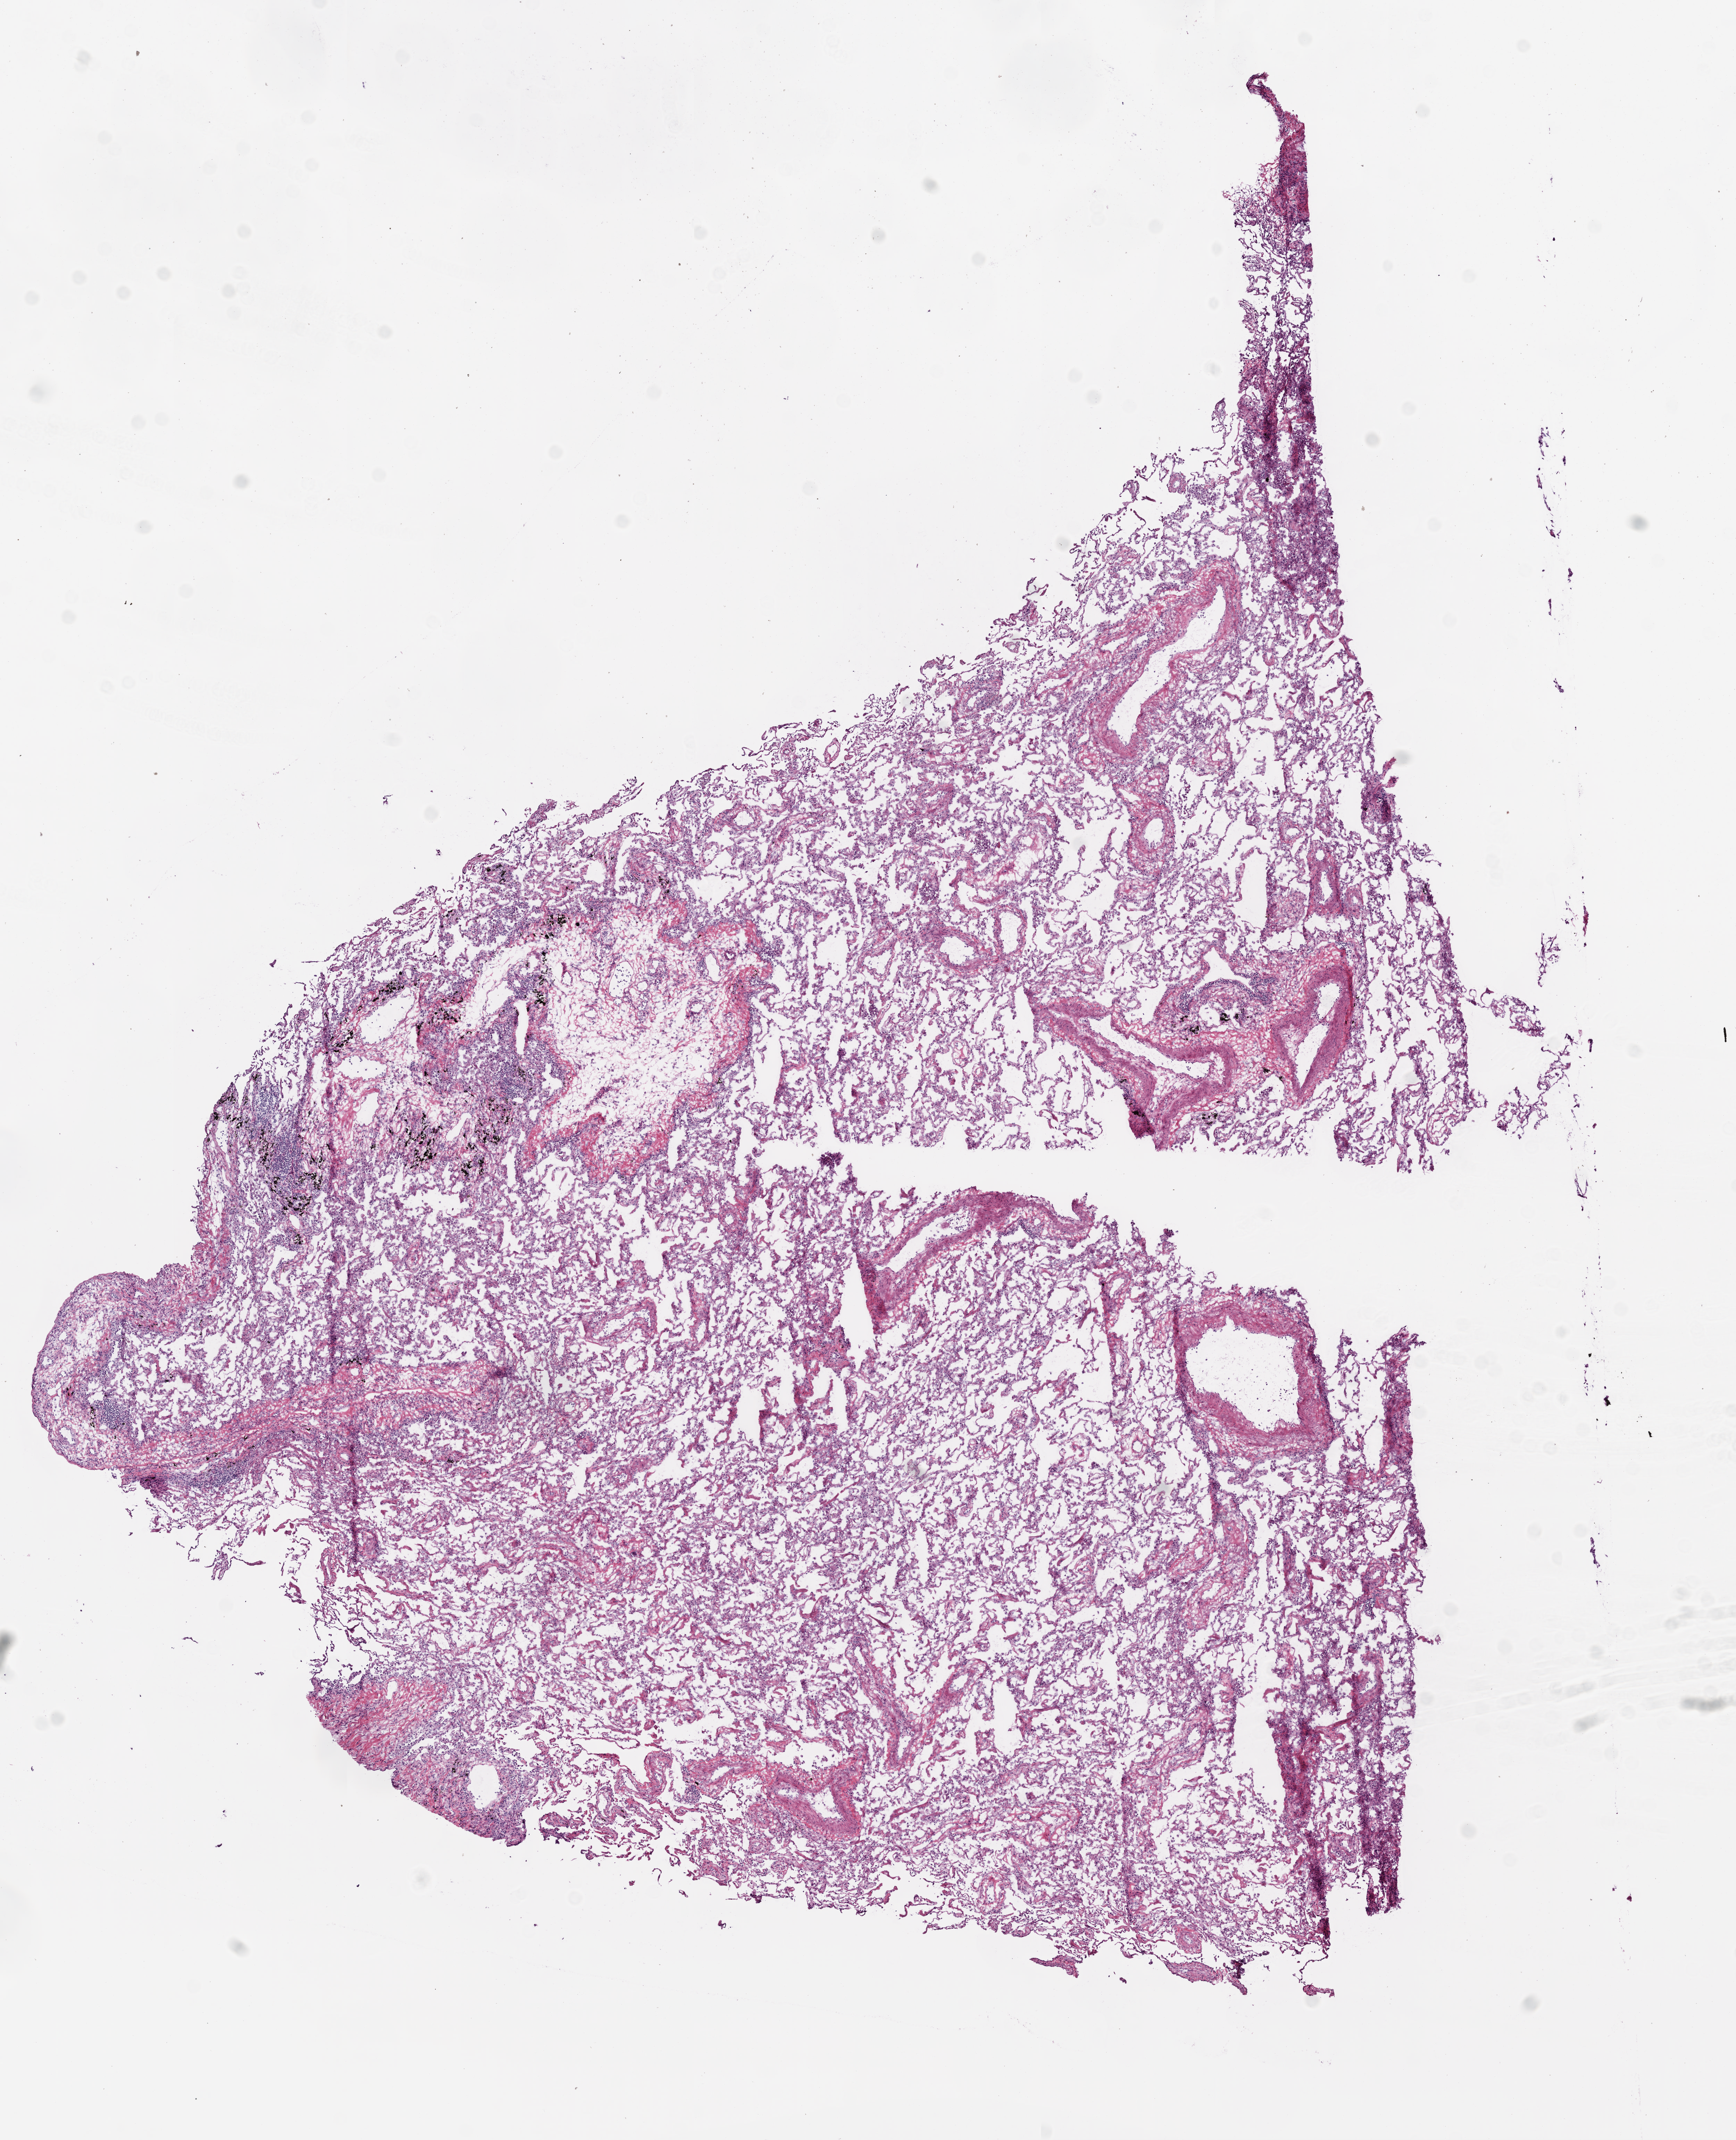
H&E-stained whole-slide image, low-resolution overview of the scanned area, about 10.0 x 12.4 mm (from a 20x scan). Frozen section from the bottom of the tissue portion. Sample: solid tissue normal (non-tumour tissue), lung. Male, age 73 years at initial diagnosis.
* this section: solid tissue normal sample (biorepository sample class)
* patient diagnosis: Squamous cell carcinoma, NOS (upper lobe, lung)